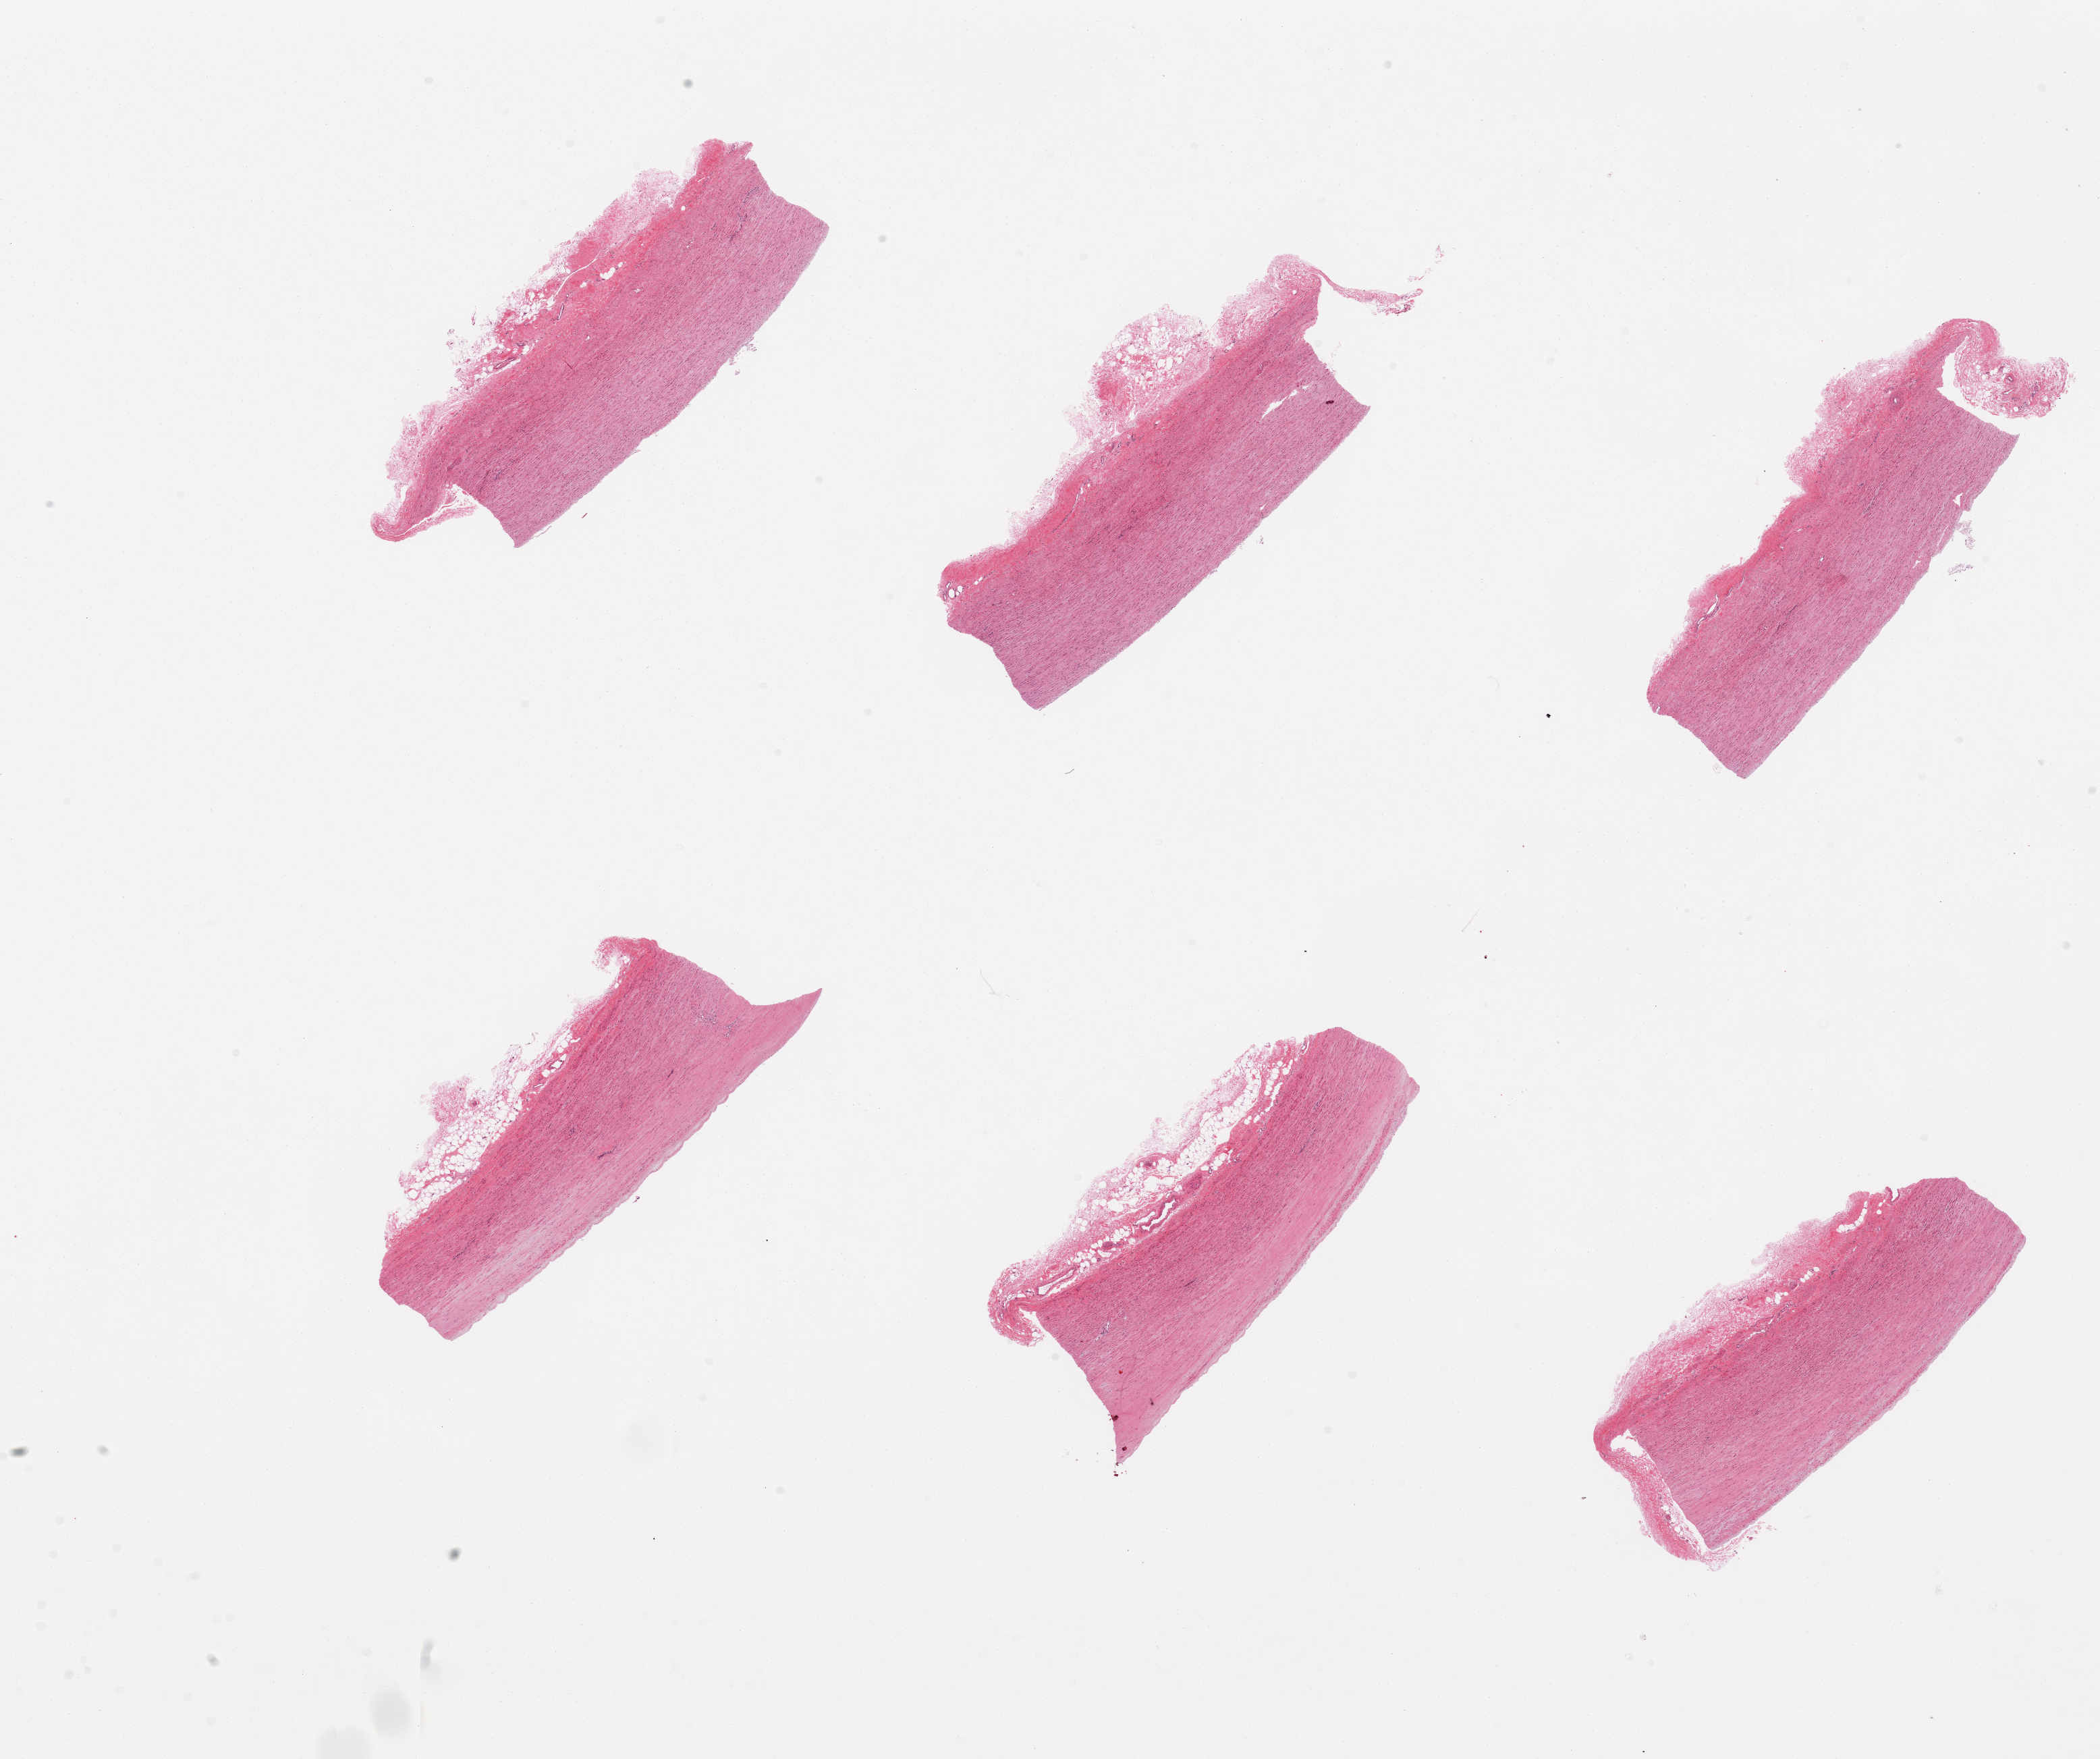
Digitized haematoxylin and eosin-stained section, brightfield — whole scanned area (about 24.6 x 20.6 mm, from a 20x scan) shown as a low-resolution overview, PAXgene-fixed paraffin-embedded (PFPE) section, target tissue: aorta, tissue donor sample. Male donor.
* review note (as recorded): 6 pieces; up to 0.7mm adventitial fat